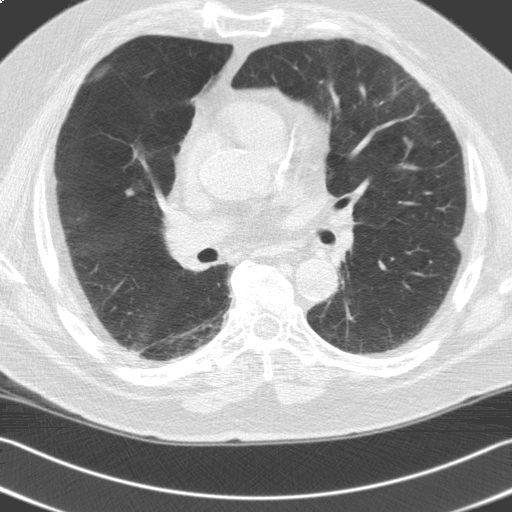
Low-dose screening chest CT, one axial slice; slice 90 of 162 in the series (ordered by position); 120 kVp; lung window (W 1500 / L -600 HU); 3.2 mm slice thickness; 512 × 512 image matrix.
Annotated regions visible in this slice (manually delineated by an expert):
- lesion 1 (tumor, upper lobe of right lung): bounding box [x1, y1, x2, y2] px = [125, 188, 136, 199]